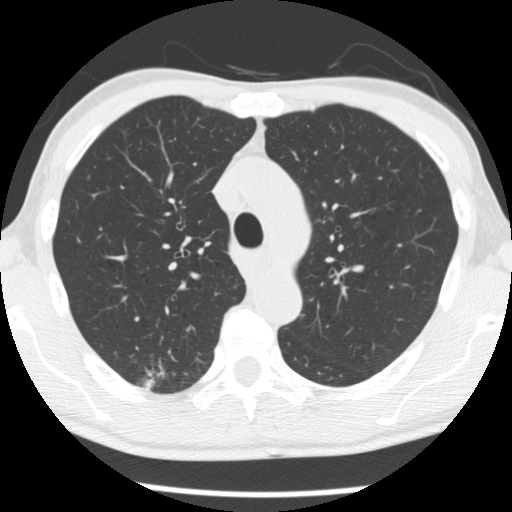
Axial slice from a low-dose chest CT screening exam. Baseline annual screen. Lung window (W 1500 / L -600 HU). 2.5 mm slice thickness. Standard (soft-tissue) reconstruction kernel (STANDARD). Slice 81 of 277 in the series. Male participant, aged 66 years at enrolment. Former smoker at enrolment.
Expert reader's lesion annotation, bounding box [x1, y1, x2, y2] px = [133, 356, 189, 399]. The screening reader recorded 4 non-calcified nodules or masses ≥4 mm on this exam (right upper lobe, right upper lobe, right upper lobe, left lower lobe); which of them this box marks is not recorded. Official screen result: positive, change unspecified: nodule(s) >= 4 mm or enlarging nodule(s), mass(es), or other non-specific abnormalities suspicious for lung cancer. Later outcome: lung cancer diagnosed 503 days after this screen (after the second annual screen) — adenocarcinoma, NOS, right upper lobe, undifferentiated (G4), stage IA (AJCC 6th edition), 20 mm at pathology.